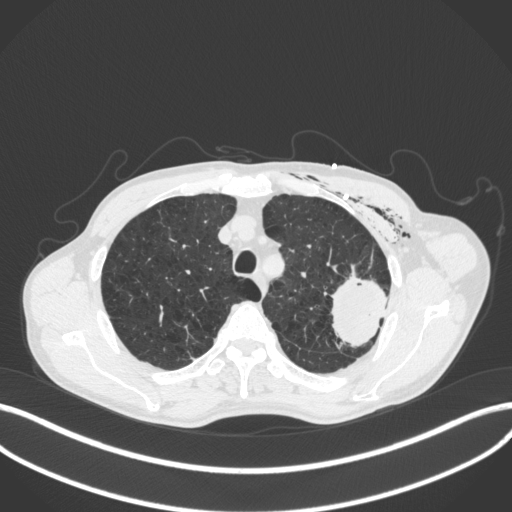
Chest CT, one axial slice; slice 319 of 416 in the series (ordered by position); lung window (W 1500 / L -600 HU); 1 mm slice thickness; 512 × 512 image matrix, field of view 400 × 400 mm. Male patient, age 58 years. From the clinical record (not read from this slice): clinical TNM (as recorded): T3 N0 M0.
Outlined on this slice (bounding box drawn by a radiologist):
- lung tumour (recorded histology: adenocarcinoma): bounding box (x1, y1, x2, y2) in pixels: (324, 263, 391, 352)